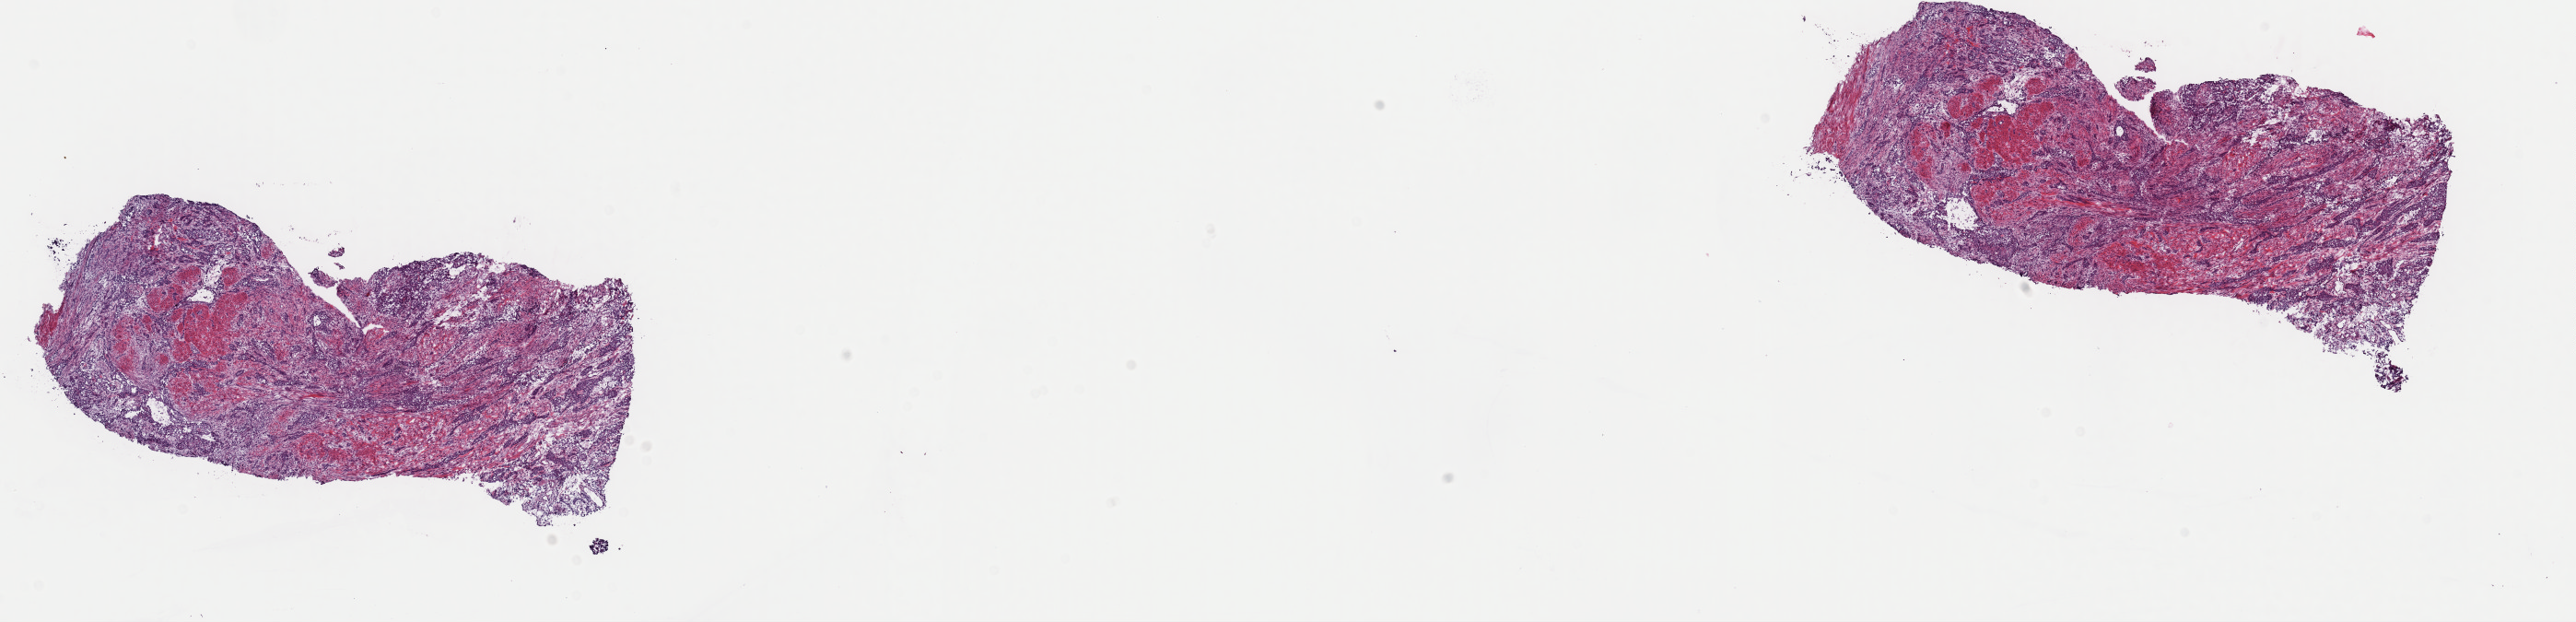
Whole-slide histology image, Hematoxylin and eosin (H&E) stained — whole scanned area (about 22.1 x 5.3 mm) shown as a low-resolution overview, frozen section from the top of the tissue portion, primary tumour sample from the bladder. Female, age 60 years at initial diagnosis. Histologic grade: high grade. Slide review estimates, as recorded: tumour cells 75%, tumour nuclei 75%, normal cells 0%, stromal cells 25%, necrosis 0%. Inflammatory infiltration, as recorded: lymphocyte infiltration 4%, monocyte infiltration 2%, neutrophil infiltration 4%.
Lymph nodes positive (case pathology): 0 of 24 examined. AJCC pathologic stage: III (7th edition). TNM: T3b N0 MX. Diagnosis: Transitional cell carcinoma.